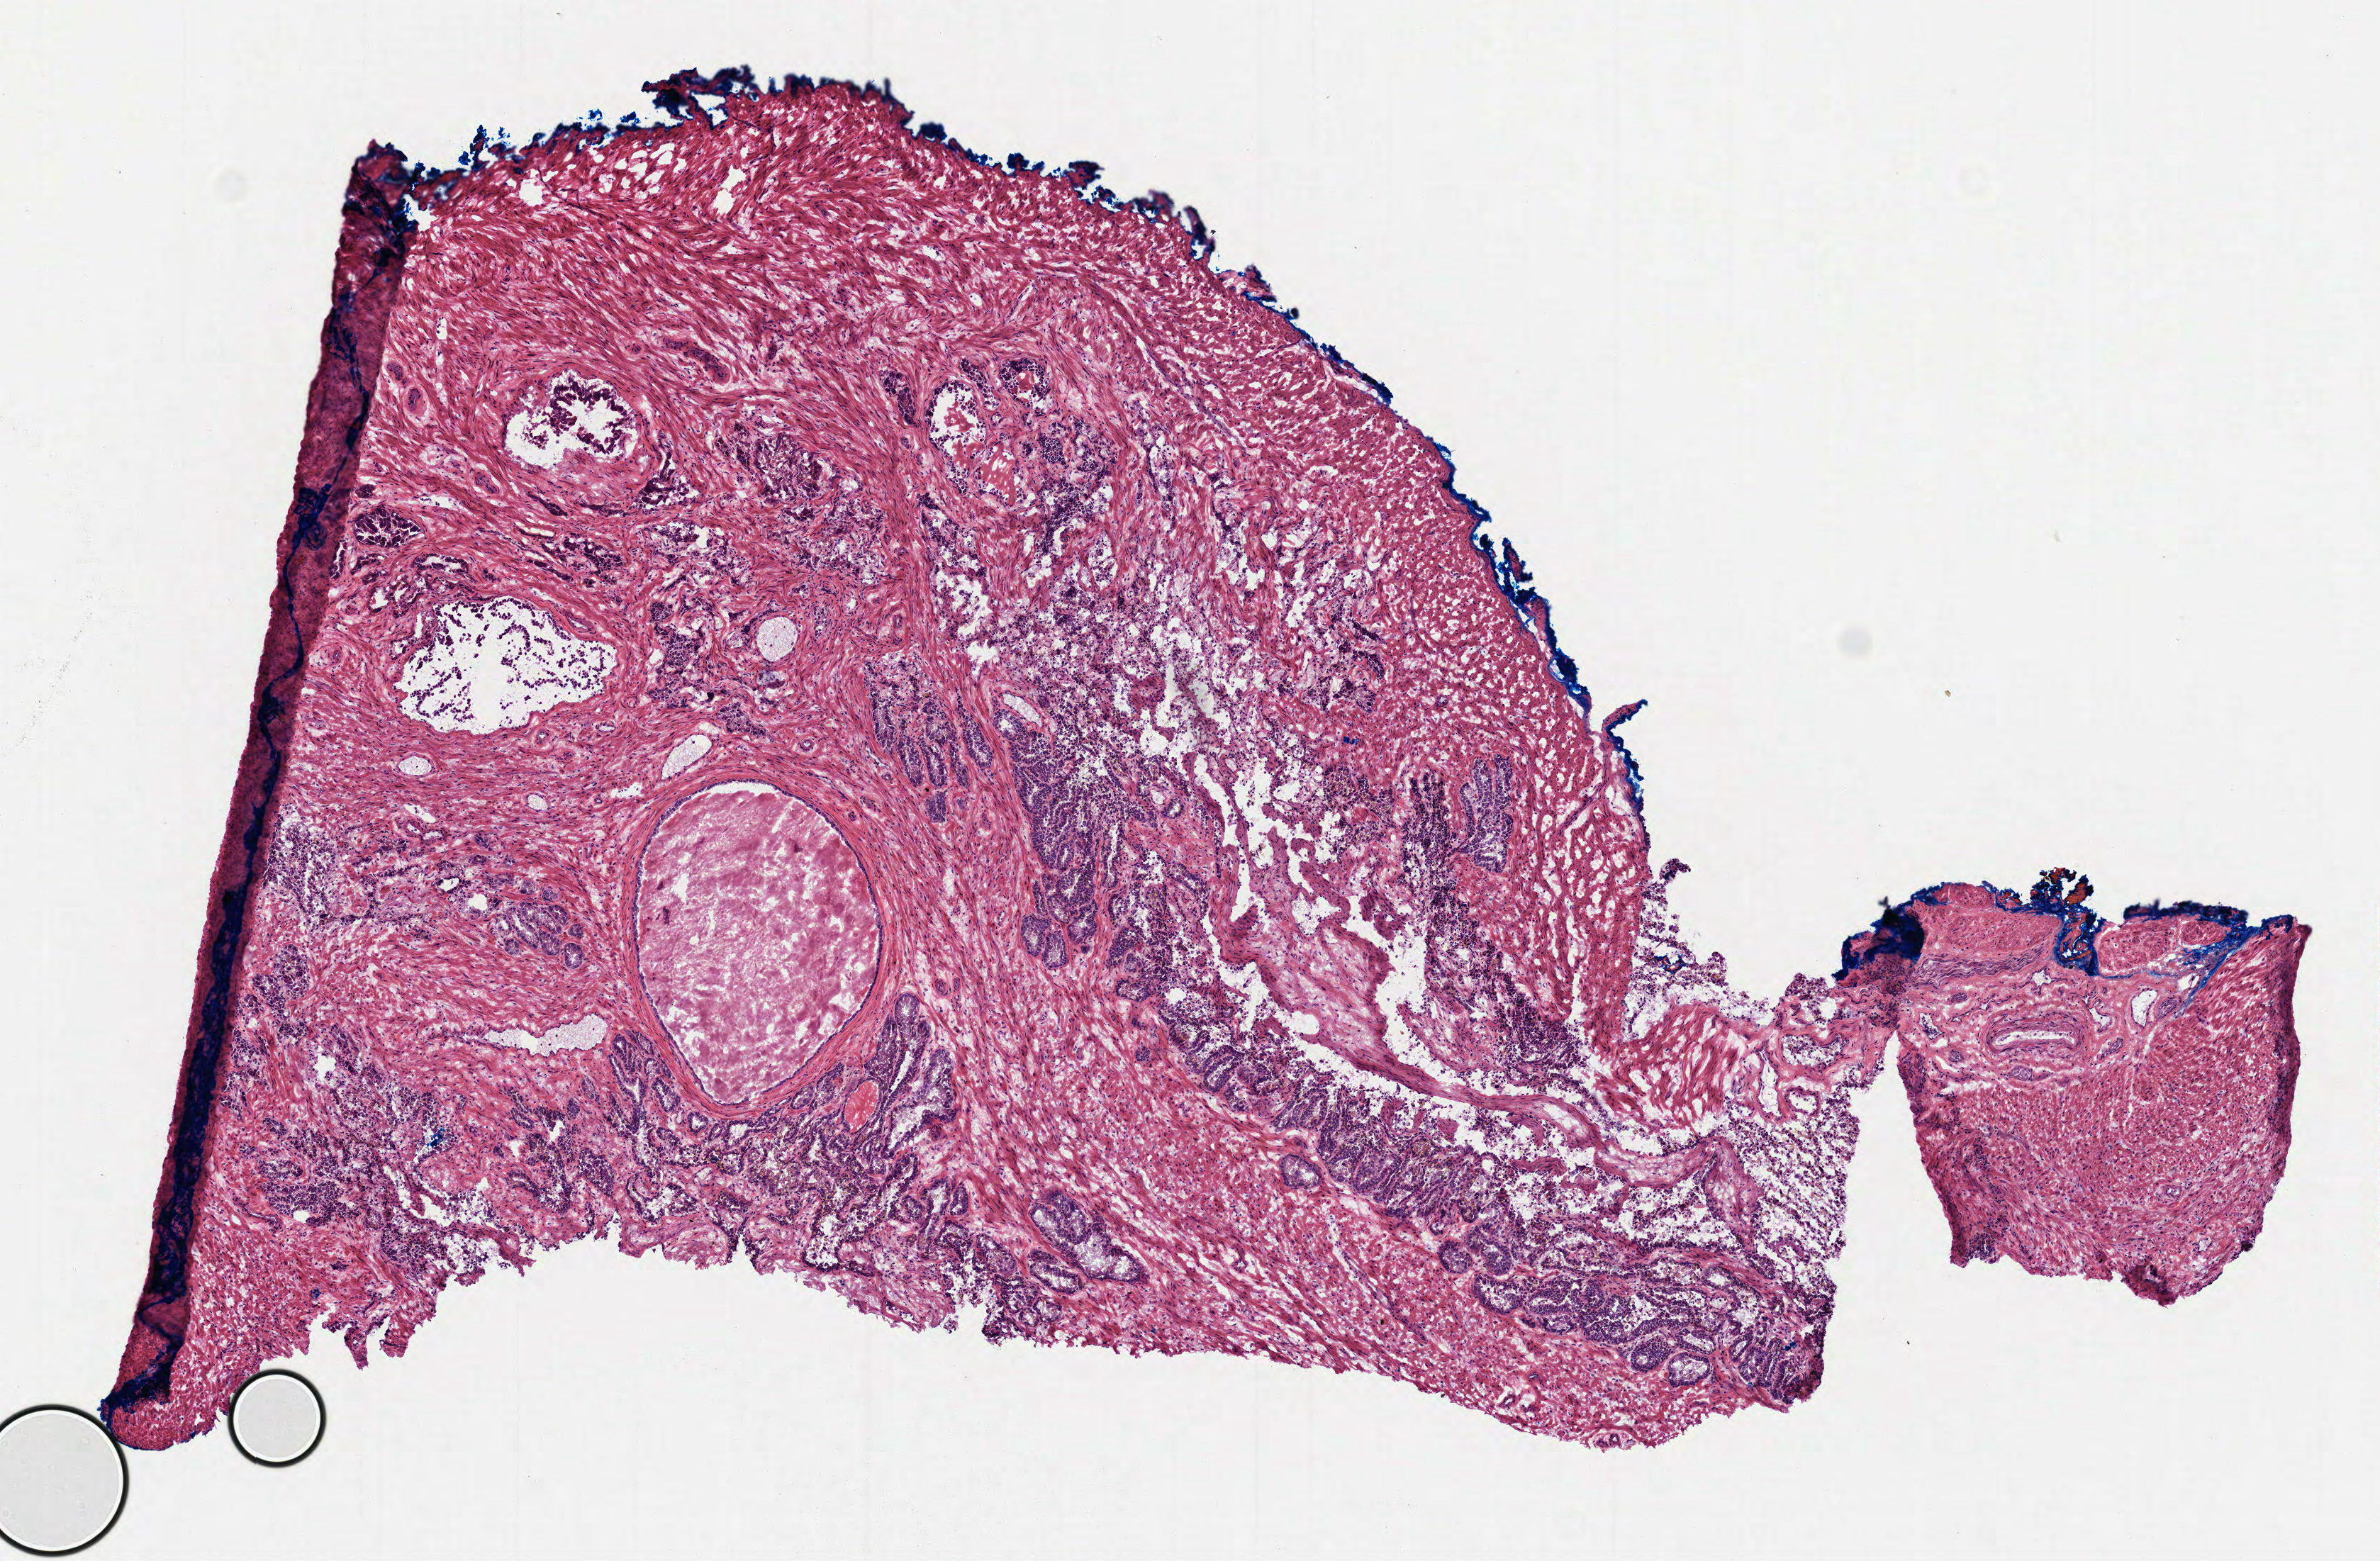
Whole-slide histology image, H&E — low-resolution overview of the scanned area, about 6.8 x 4.4 mm, frozen section, prostate, solid tissue normal (non-tumour tissue) sample. Male, age 72 years at initial diagnosis.
* this section: solid tissue normal (non-tumour) sample from the same patient
* patient diagnosis: Acinar cell carcinoma (prostate gland)